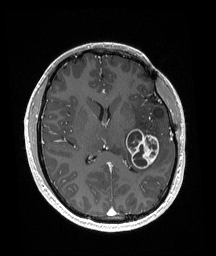
Brain MRI from a brain-tumour surgery series, one axial slice. Position 85 of 192 along the scan axis. T1-weighted post-contrast. 1 mm slice thickness. 216 × 256 image matrix, field of view 211 × 250 mm. Case-level facts recorded for this patient, not image findings: histopathology: Glioneuronal tumor; WHO grade: 2; tumour location: Left Superior Temporal Gyrus.
Structures marked on this image (manually delineated by an expert):
- tumour: bounding box <126,129,160,169> (left, top, right, bottom; pixels)